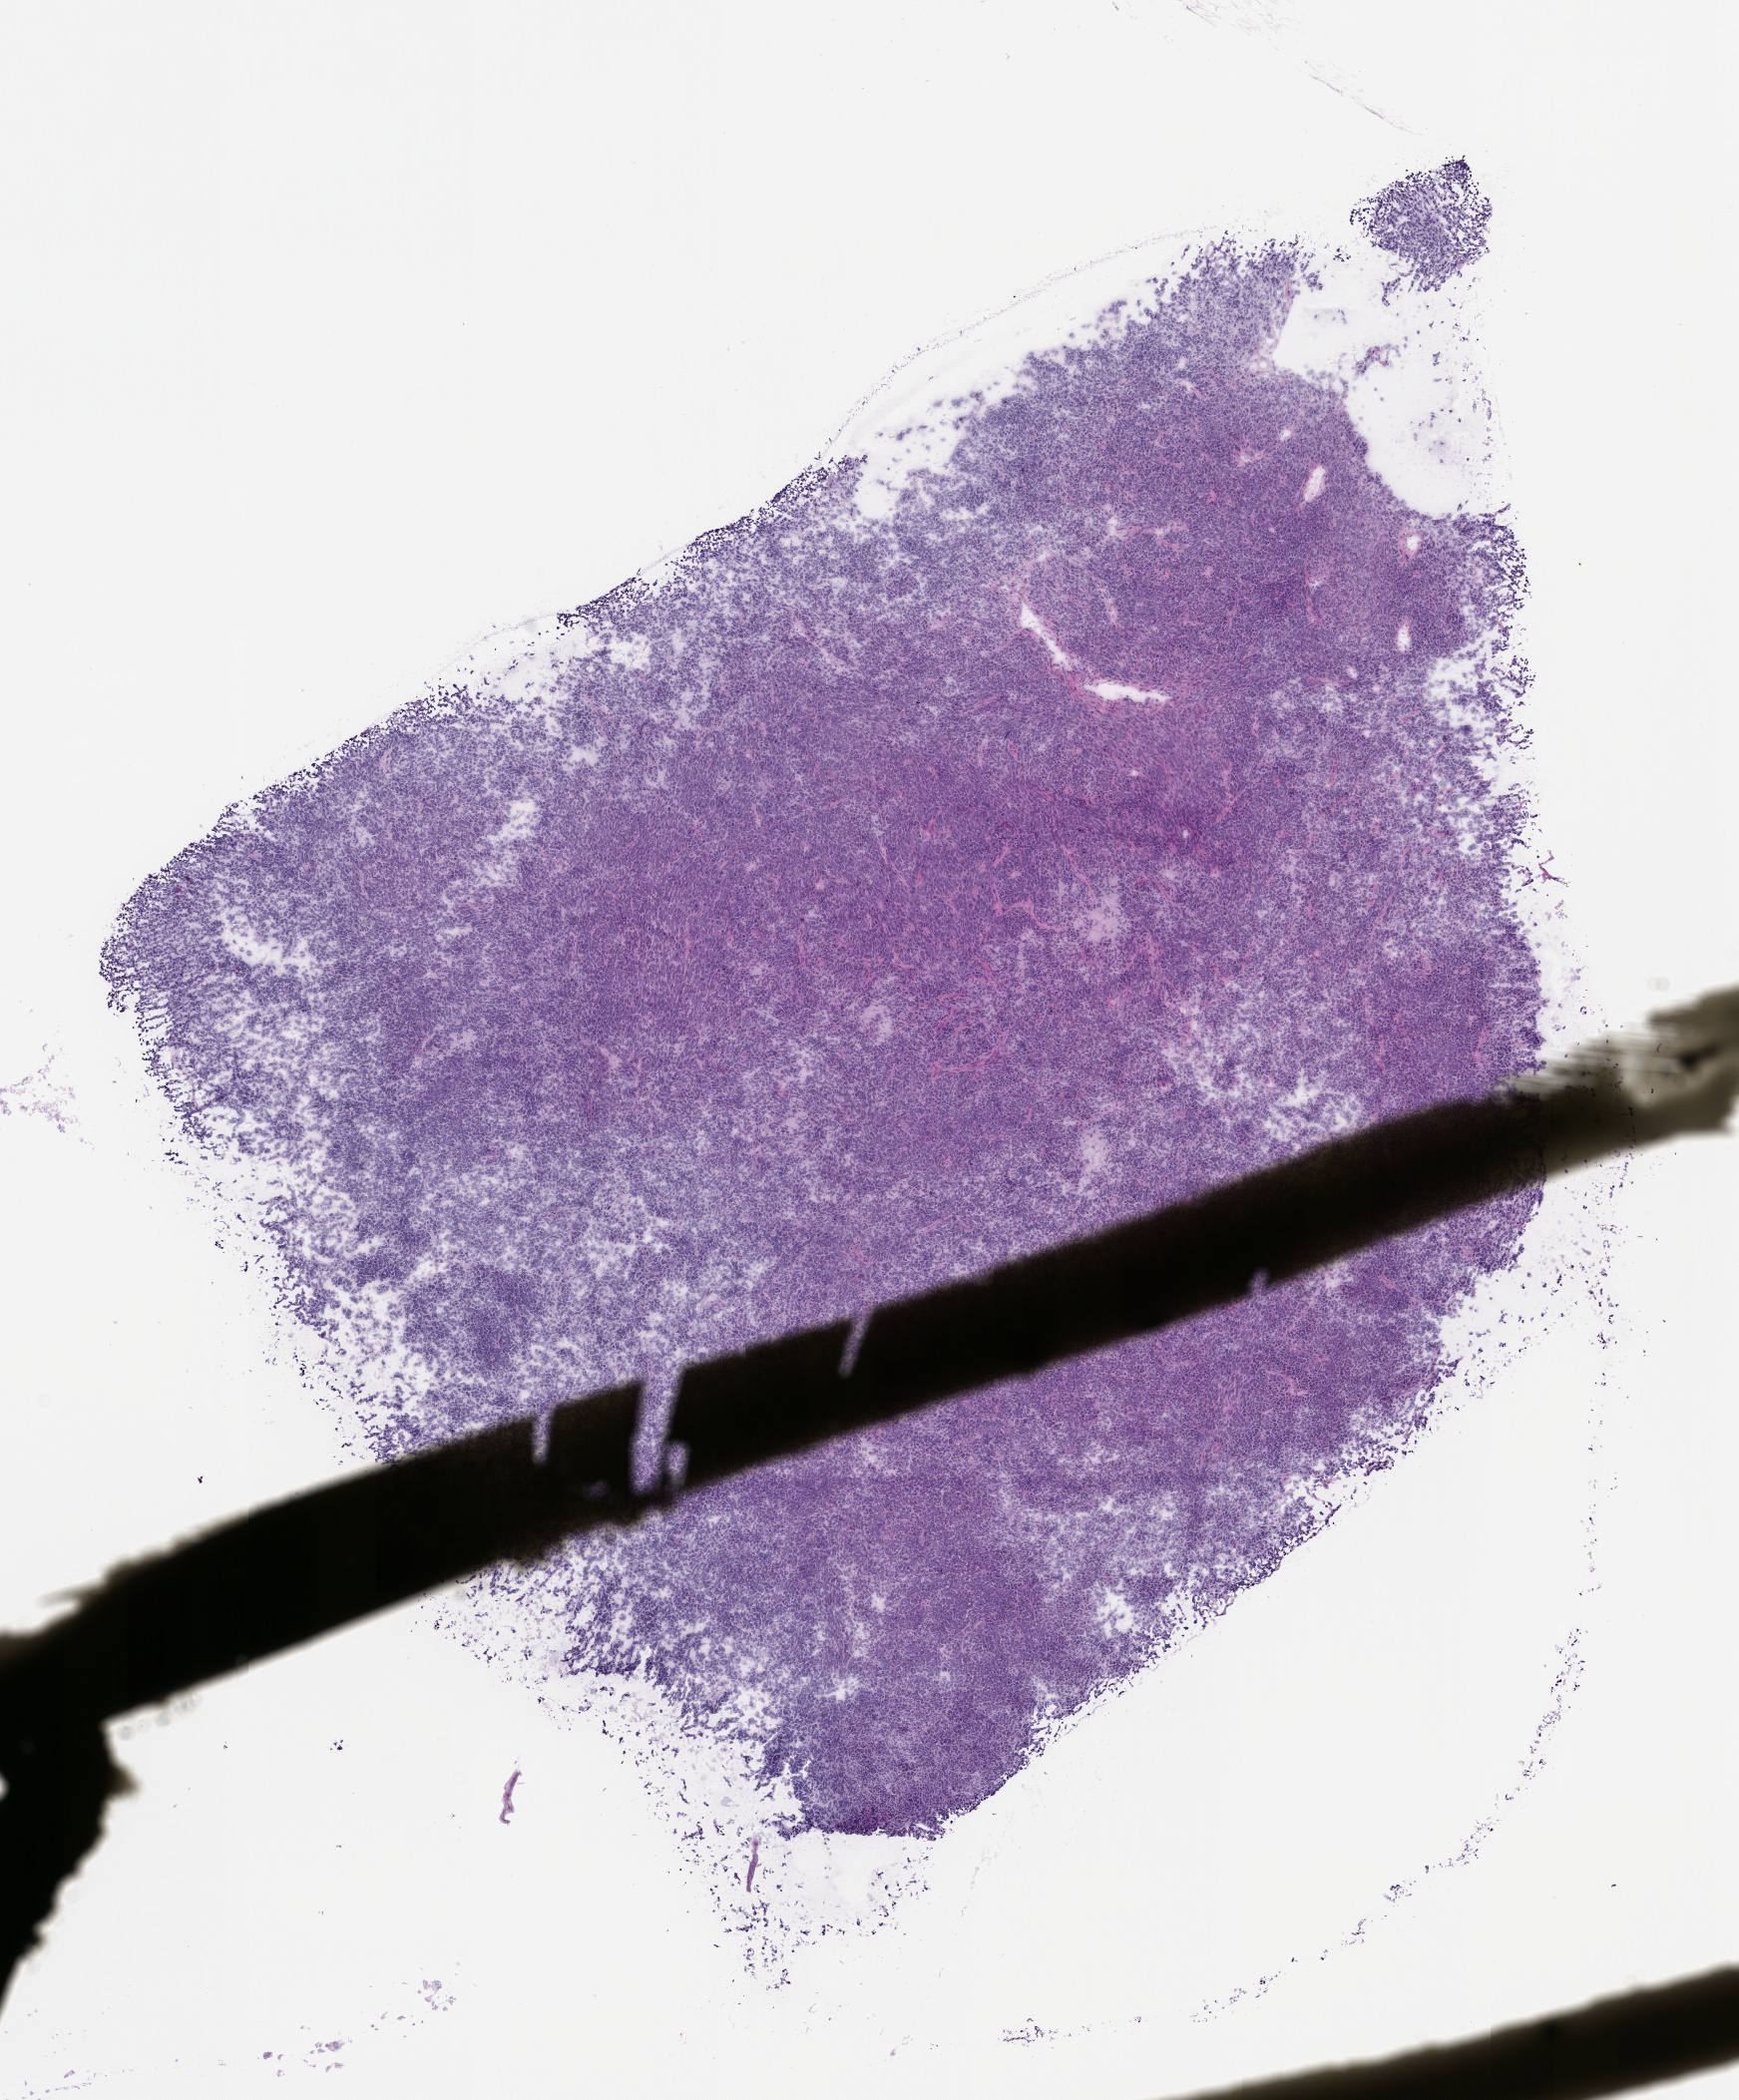
Digitized hematoxylin and eosin (H&E)-stained section of the patient's (originator) tumor tissue, shown as a low-resolution overview of the whole scanned area (about 7.0 x 8.5 mm). Formalin-fixed, paraffin-embedded (FFPE) tissue. Originating tumor site category: musculoskeletal. Male patient, age 61 years.
Diagnosis: Spindle Cell Sarcoma.